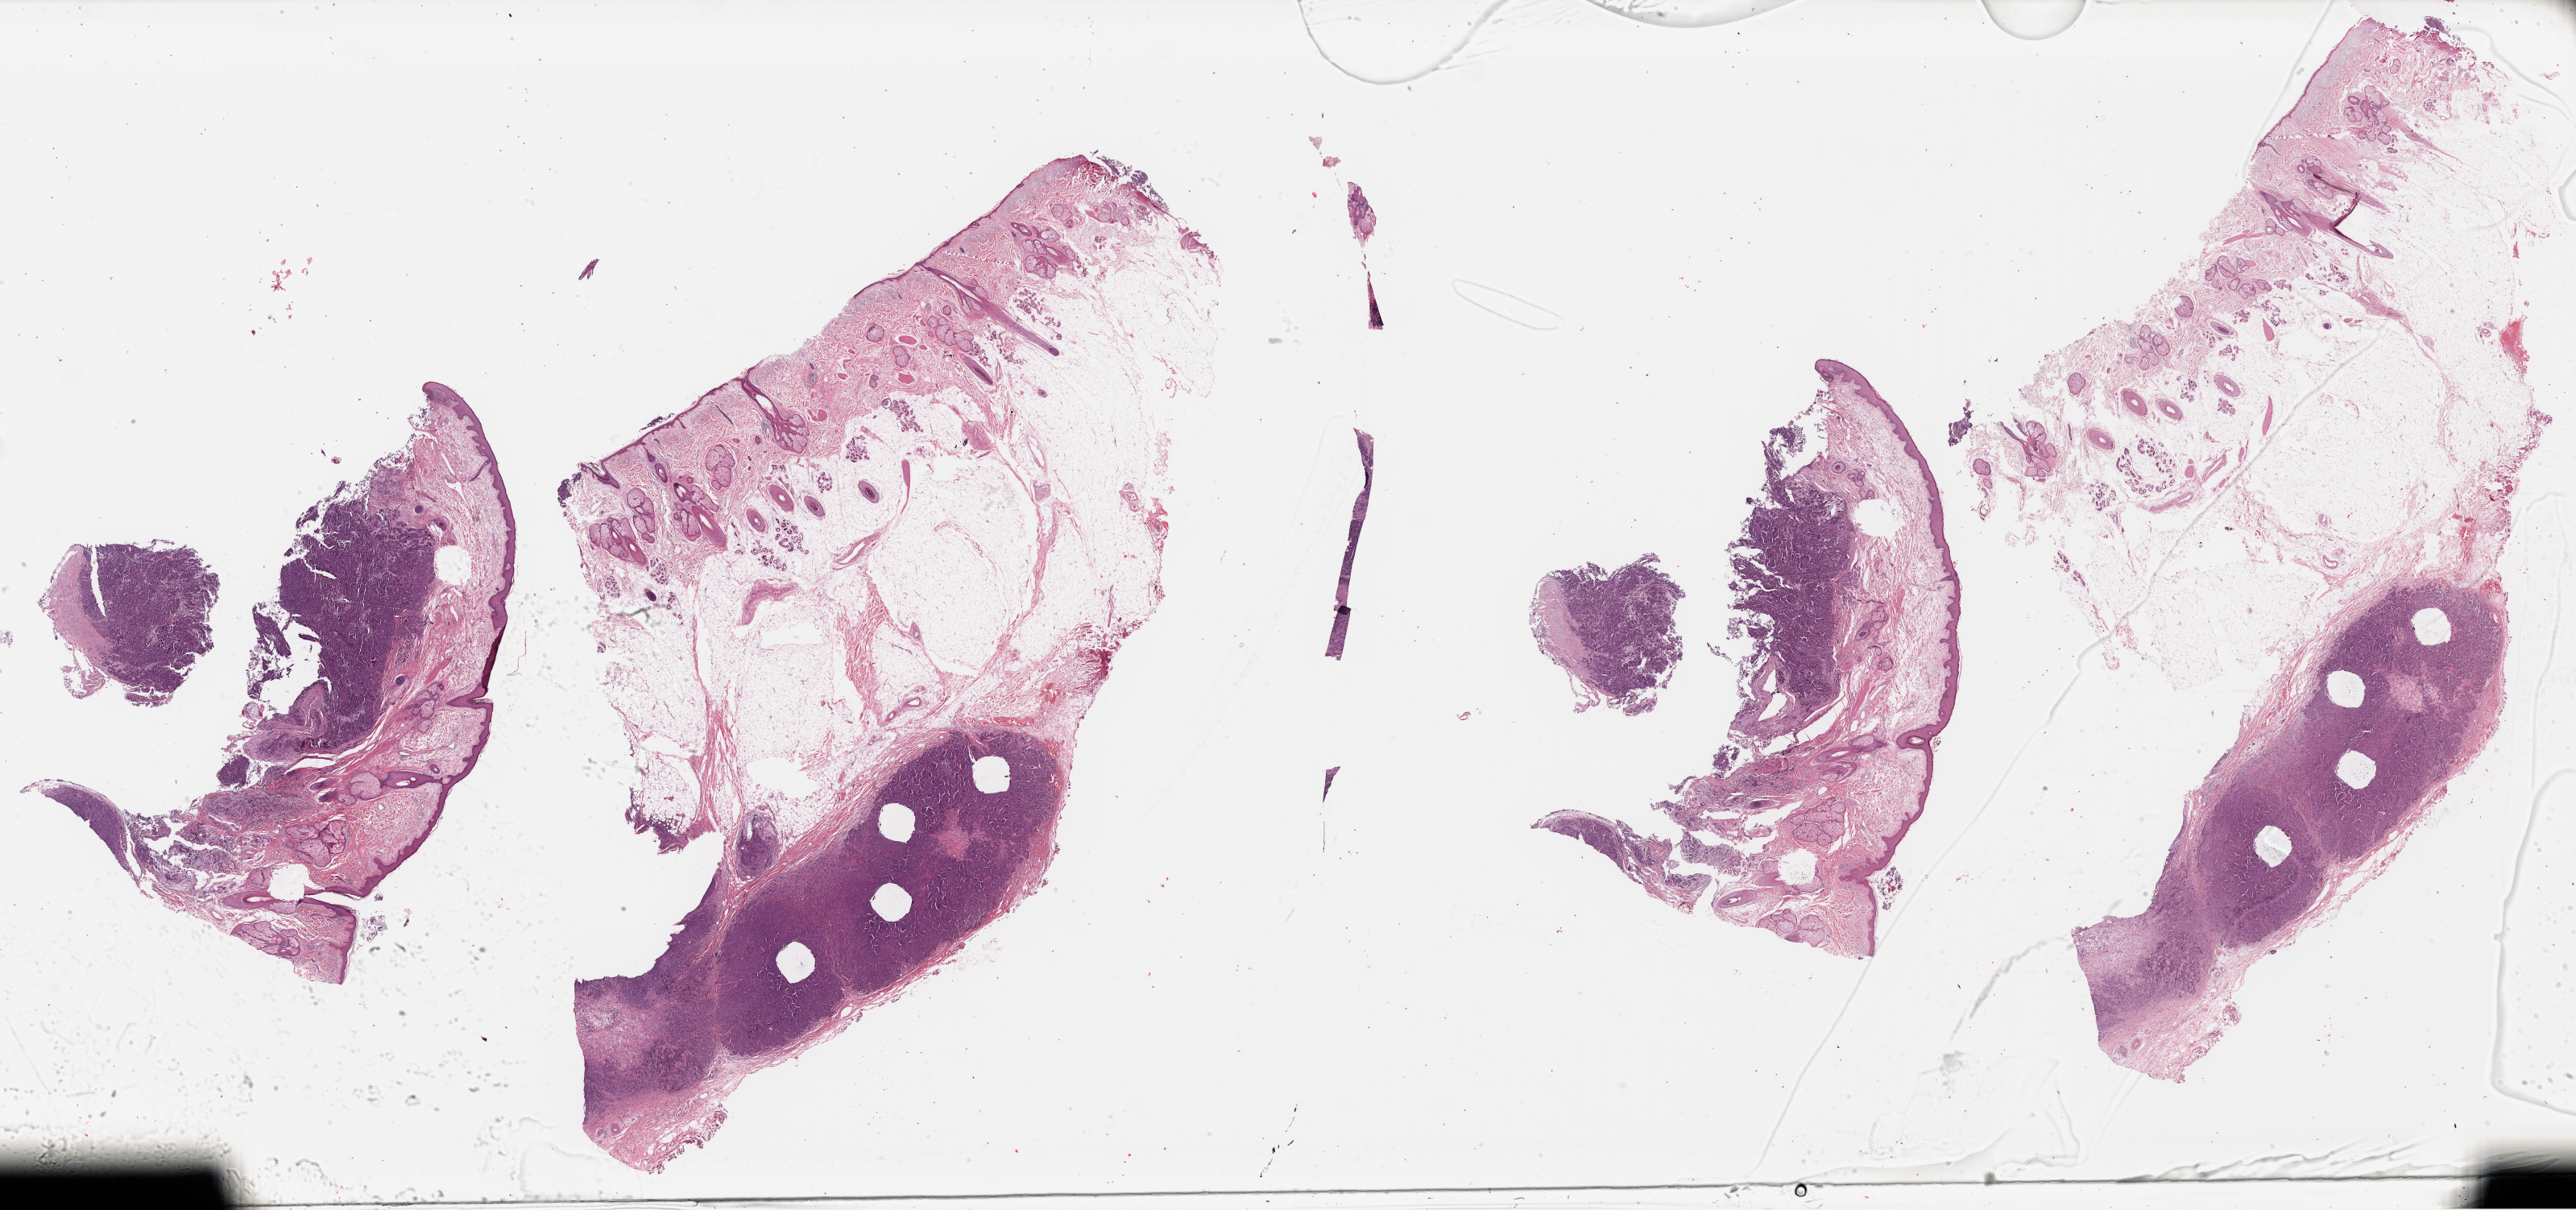
Whole-slide histology image, H&E — shown as a low-resolution overview of the whole scanned area (about 50.3 x 23.6 mm, from a 40x scan), formalin-fixed paraffin-embedded (FFPE) diagnostic section, metastatic tumour sample, sampled site: skin. Male, age 51 years at initial diagnosis.
This section: metastatic tumour tissue. Patient diagnosis: Malignant melanoma, NOS.